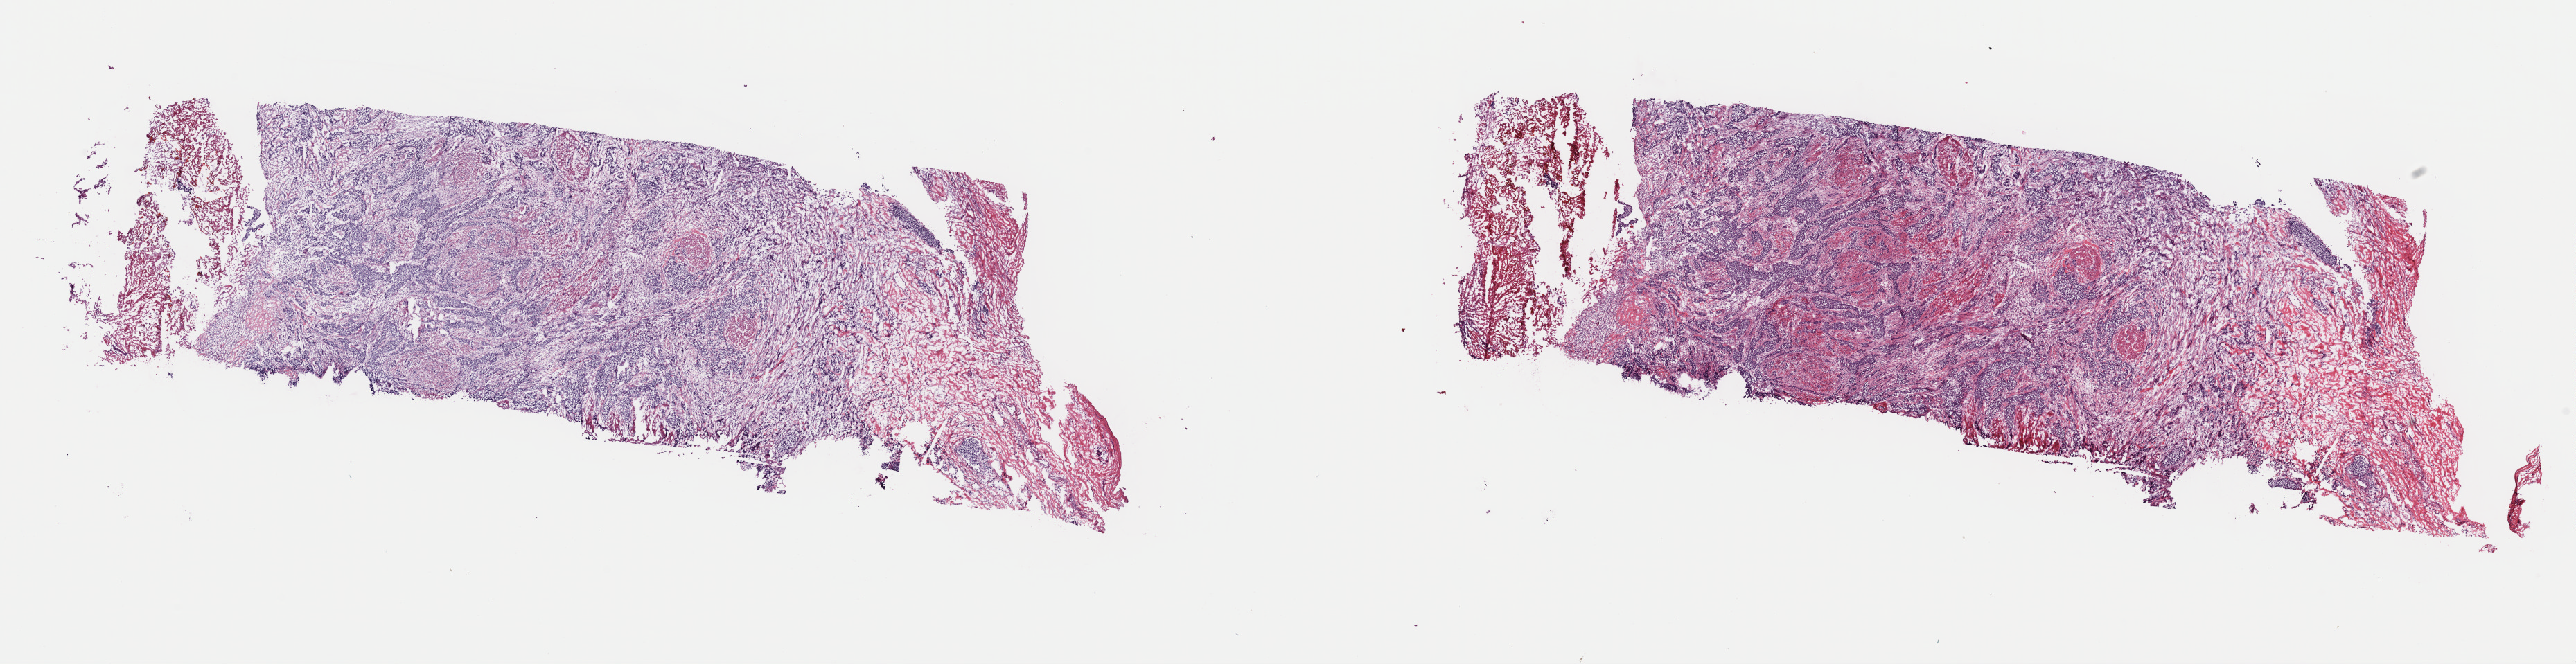
Digitized H&E tissue section (whole slide) — whole scanned area (about 29.4 x 7.6 mm, from a 40x scan) shown as a low-resolution overview. Frozen section from the top of the tissue portion. Bladder, primary tumour sample. Female, age 79 years at initial diagnosis. Histologic grade: high grade. Slide review estimates, as recorded: tumour cells 35%, tumour nuclei 80%, normal cells 0%, stromal cells 55%, necrosis 10%. Inflammatory infiltration, as recorded: lymphocyte infiltration 4%, monocyte infiltration 1%, neutrophil infiltration 2%.
AJCC pathologic stage: III (7th edition). TNM: T4a N0 MX. Pathologic diagnosis: Transitional cell carcinoma (posterior wall of bladder).